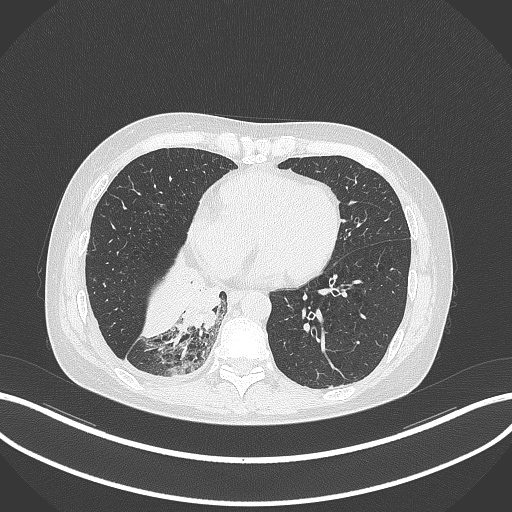
Chest CT, one axial slice. Position 104 of 329 along the scan axis. Reconstruction kernel B70f. 120 kVp. Lung window (W 1500 / L -600 HU). 1 mm slice thickness. 512 × 512 image matrix, field of view 400 × 400 mm. Patient: female, 63 years. From the clinical record (not read from this slice): clinical TNM (as recorded): T1c N0 M0.
Structures marked on this image (rectangle marked by the reading radiologist):
- lung tumour (recorded histology: adenocarcinoma): bounding box [x1, y1, x2, y2] px = [176, 284, 228, 339]